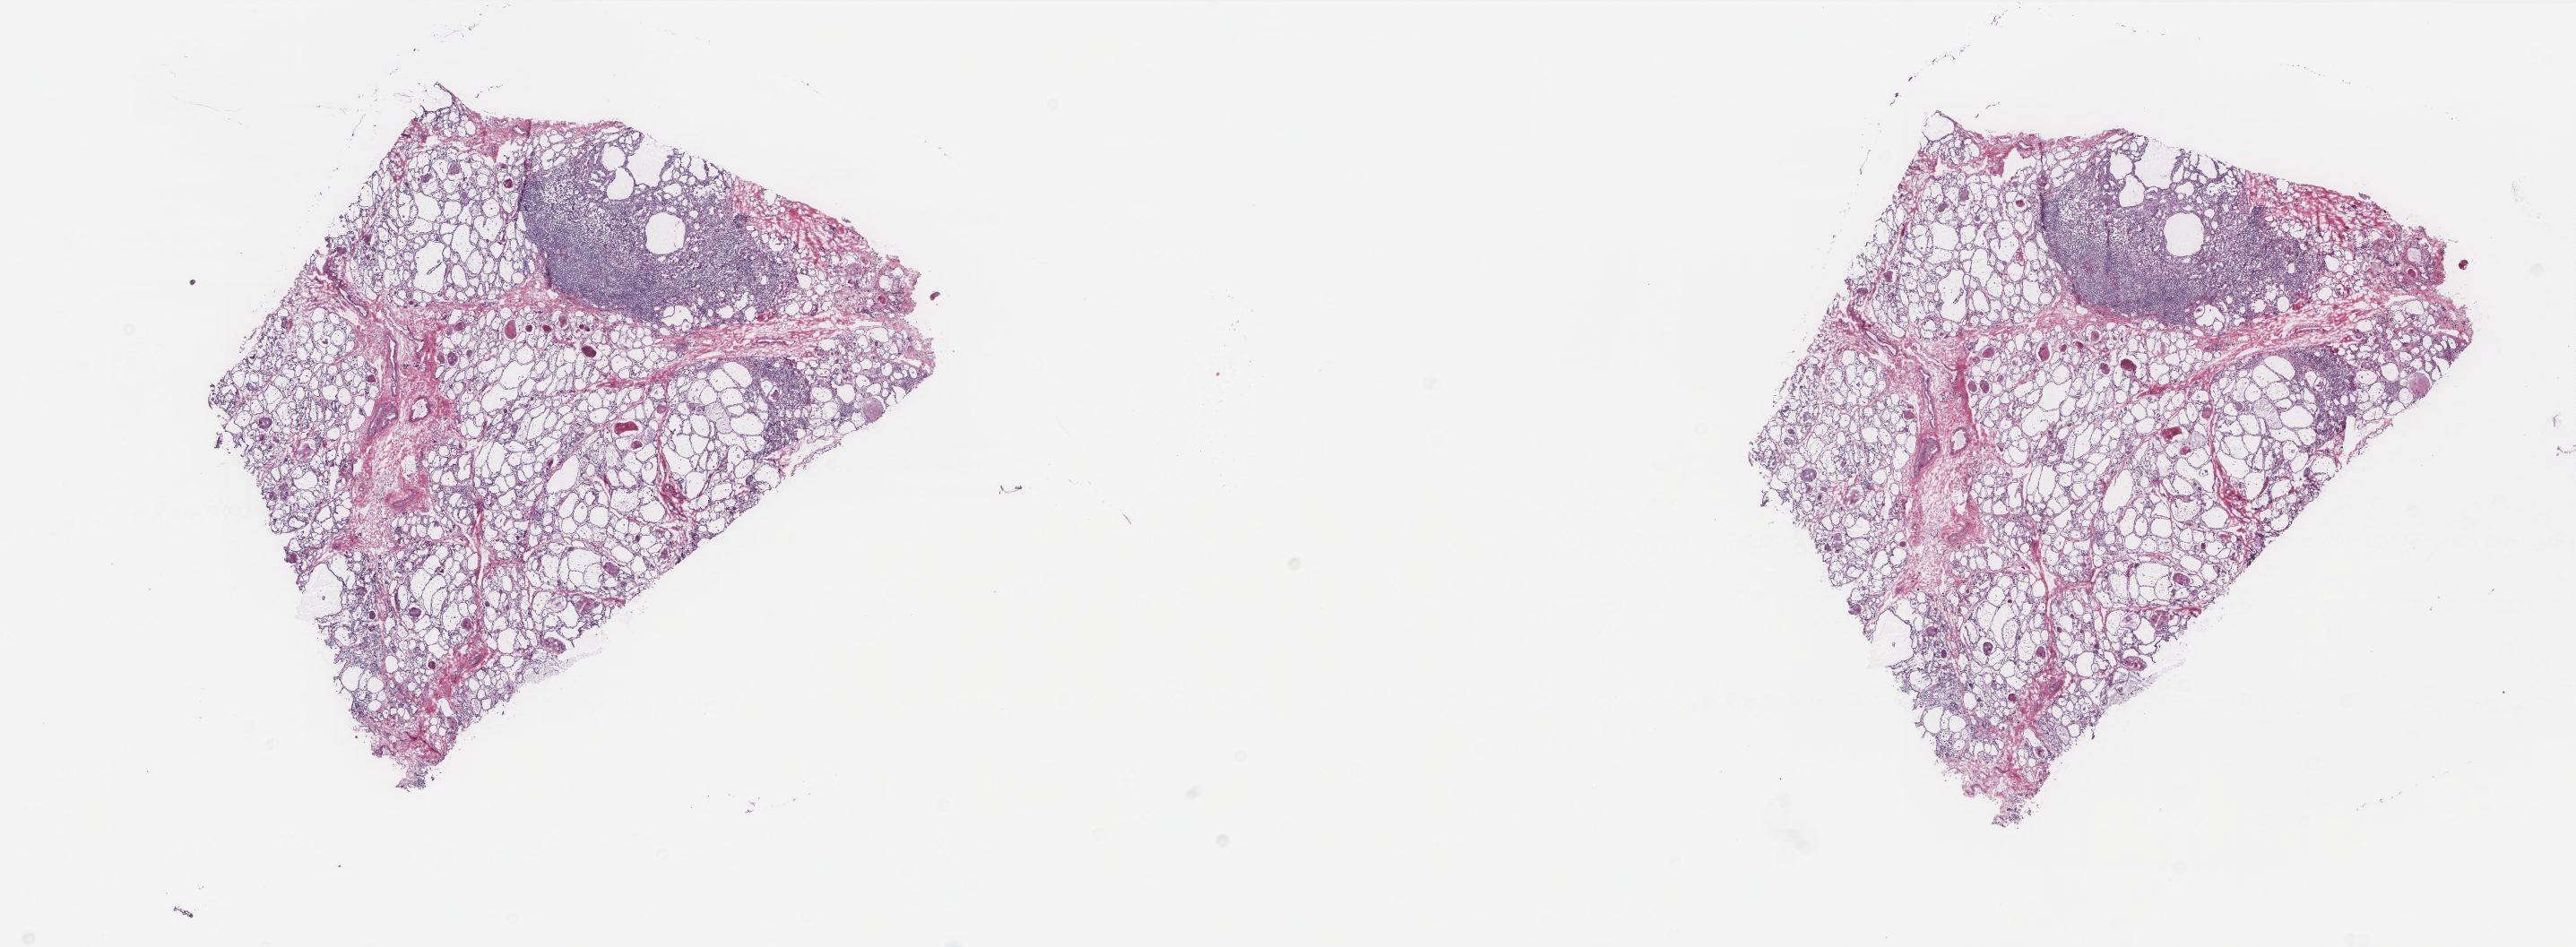
Hematoxylin and eosin (H&E) stained whole-slide image — whole scanned area (about 23.0 x 8.4 mm, acquisition: 20x scan) shown as a low-resolution overview, frozen section from the top of the tissue portion, sample: solid tissue normal (non-tumour tissue), thyroid. Female, age 69 years at initial diagnosis. Pathologist review of this section (percent, as recorded): tumour cells 0%, tumour nuclei 0%, normal cells 90%, stromal cells 10%, necrosis 0%. Inflammatory infiltration, as recorded: lymphocyte infiltration 20%, monocyte infiltration 0%, neutrophil infiltration 0%.
This section: solid tissue normal sample (biorepository sample class). Patient diagnosis: Papillary adenocarcinoma, NOS (thyroid gland).